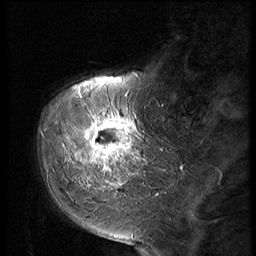
Breast MRI (dynamic contrast-enhanced), one sagittal slice. Slice 15 of 56 in the series (ordered by position). Dynamic contrast-enhanced series, image 2 of 2 at this slice position (ordered by acquisition). 1.5 T. TE 4.2 ms, TR 9 ms. 256 × 256 image matrix, field of view 180 × 180 mm. Female patient, age 51 years. Case-level facts recorded for this patient, not image findings: setting: breast cancer imaged before/during neoadjuvant chemotherapy; receptor status: triple-negative.
Annotated regions visible in this slice (semi-automatic segmentation, software-assisted and operator-edited):
- analysis volume of interest (the breast-tissue region the enhancement analysis was run in; not a lesion): box from (x=60, y=98) to (x=147, y=197) px
- tumour enhancement mask (voxels above the 140 % enhancement threshold inside the analysis volume of interest): (x=68, y=98)–(x=139, y=187)